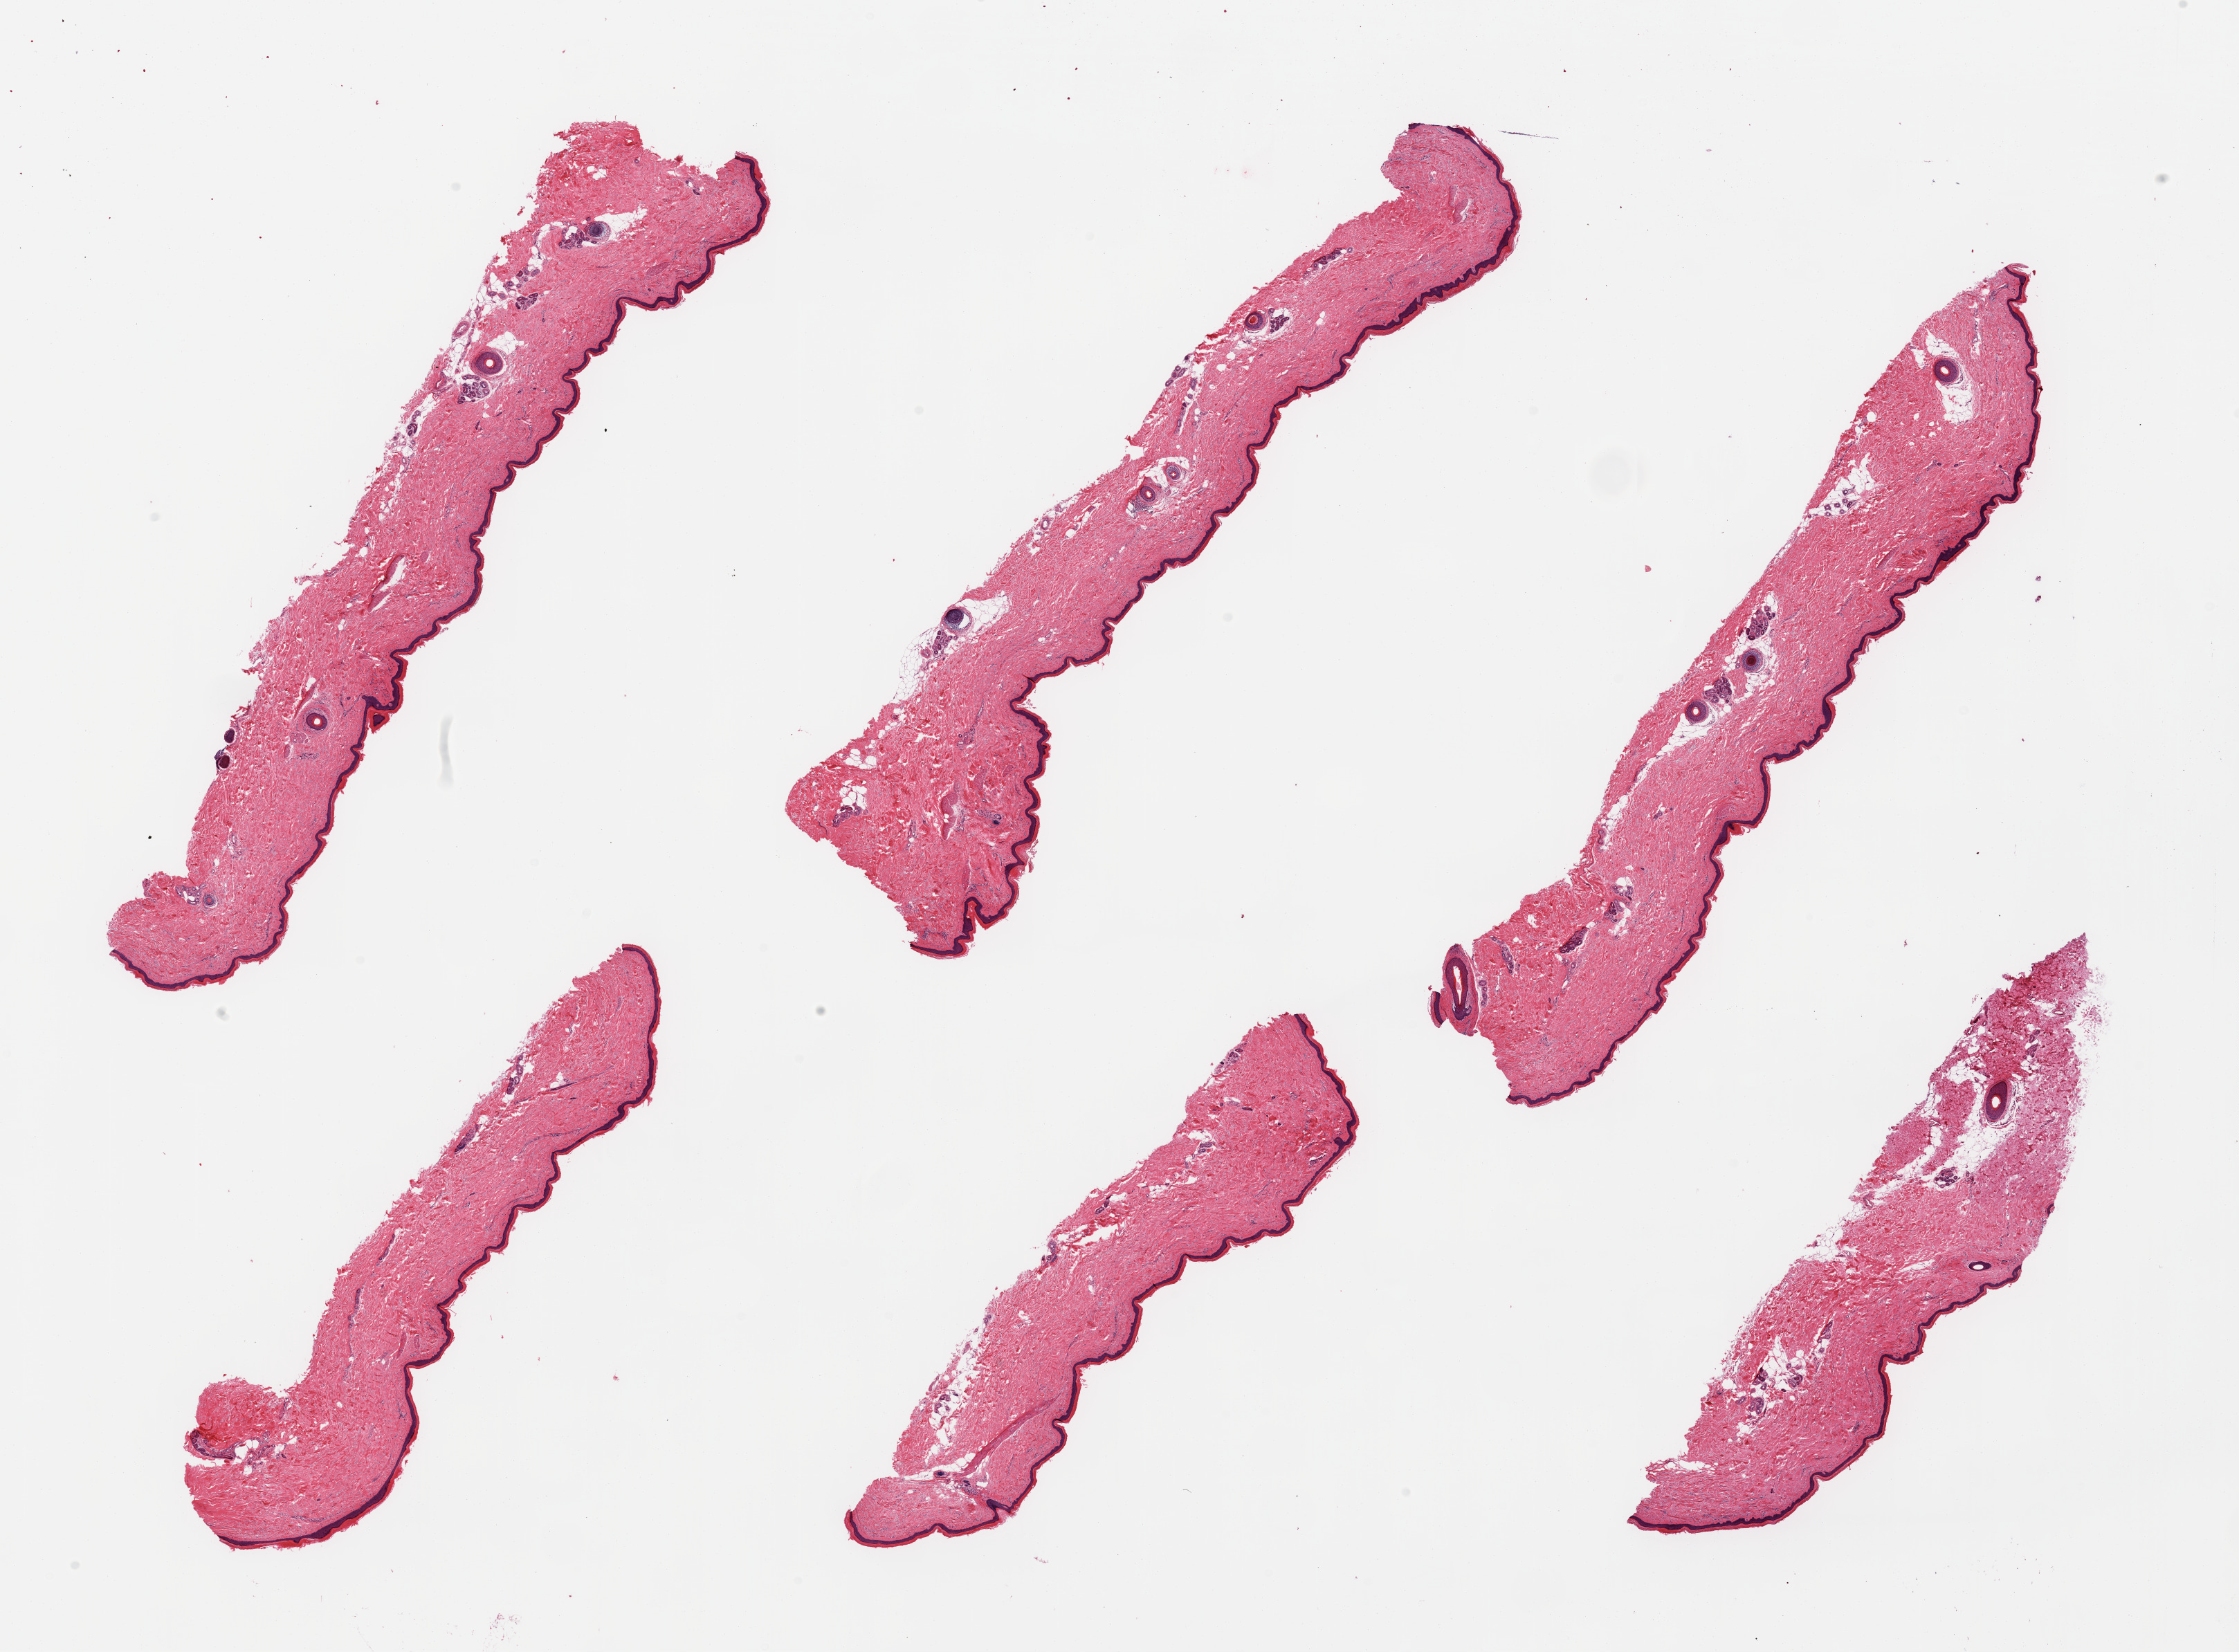
Whole-slide image, hematoxylin and eosin (H&E) stain, brightfield — a low-resolution overview of the entire scanned area, about 25.6 x 18.9 mm; PAXgene-fixed, paraffin-embedded tissue; target tissue: skin of lower leg; donor tissue sample.
Review note (as recorded): 1 piece; not adipose tissue, skin.